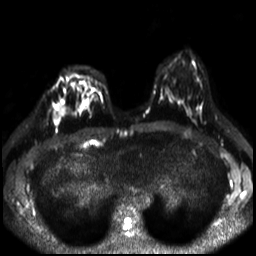
Breast MRI, one axial slice. Position 12 of 30 along the scan axis. Diffusion-weighted series; image 2 of 4 stored at this slice position (different b-values; order by instance number). 3 T. 4 mm slice thickness. 256 × 256 image matrix, field of view 320 × 320 mm. Female patient.
Structures marked on this image (expert manual segmentation):
- tumour on diffusion-weighted imaging: box from (x=55, y=100) to (x=64, y=124) px